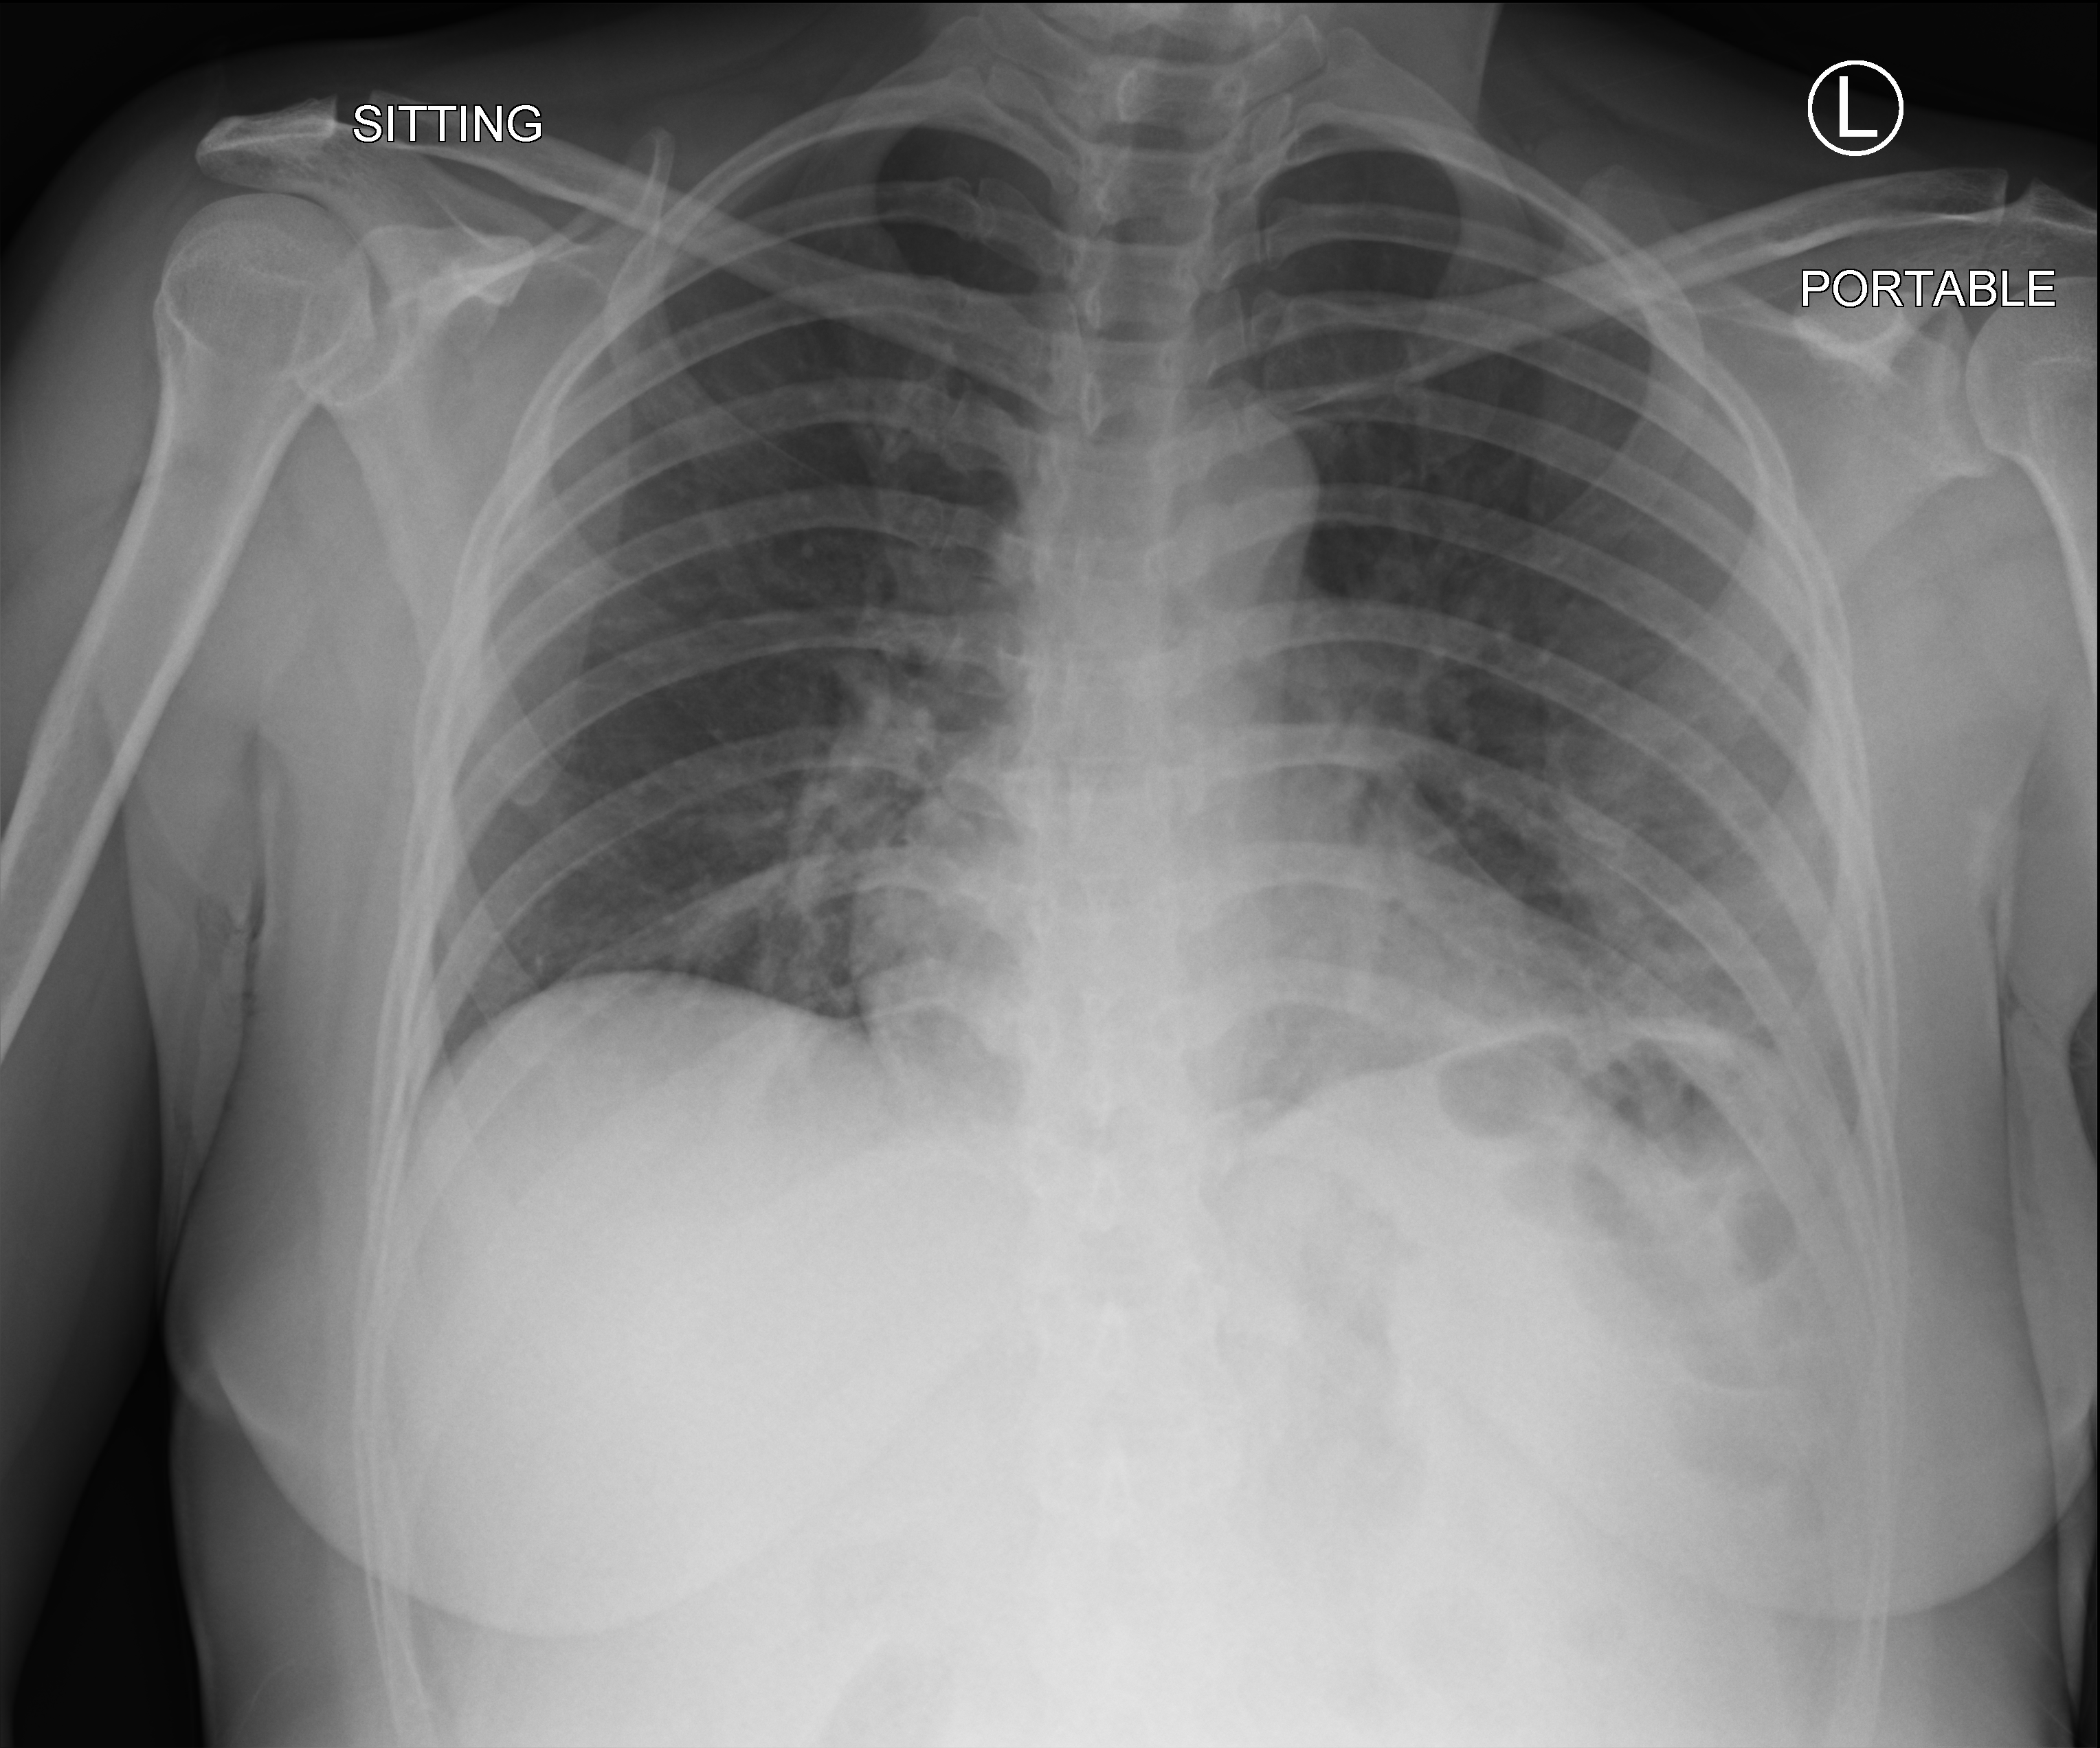
Bedside chest radiograph (computed radiography). Female patient hospitalised with COVID-19, age 18–59 years.
Admission-level facts for this patient (not findings on this image; timing relative to this image not recorded):
- length of hospital stay: 1 day
- mechanically ventilated during this hospital stay: no